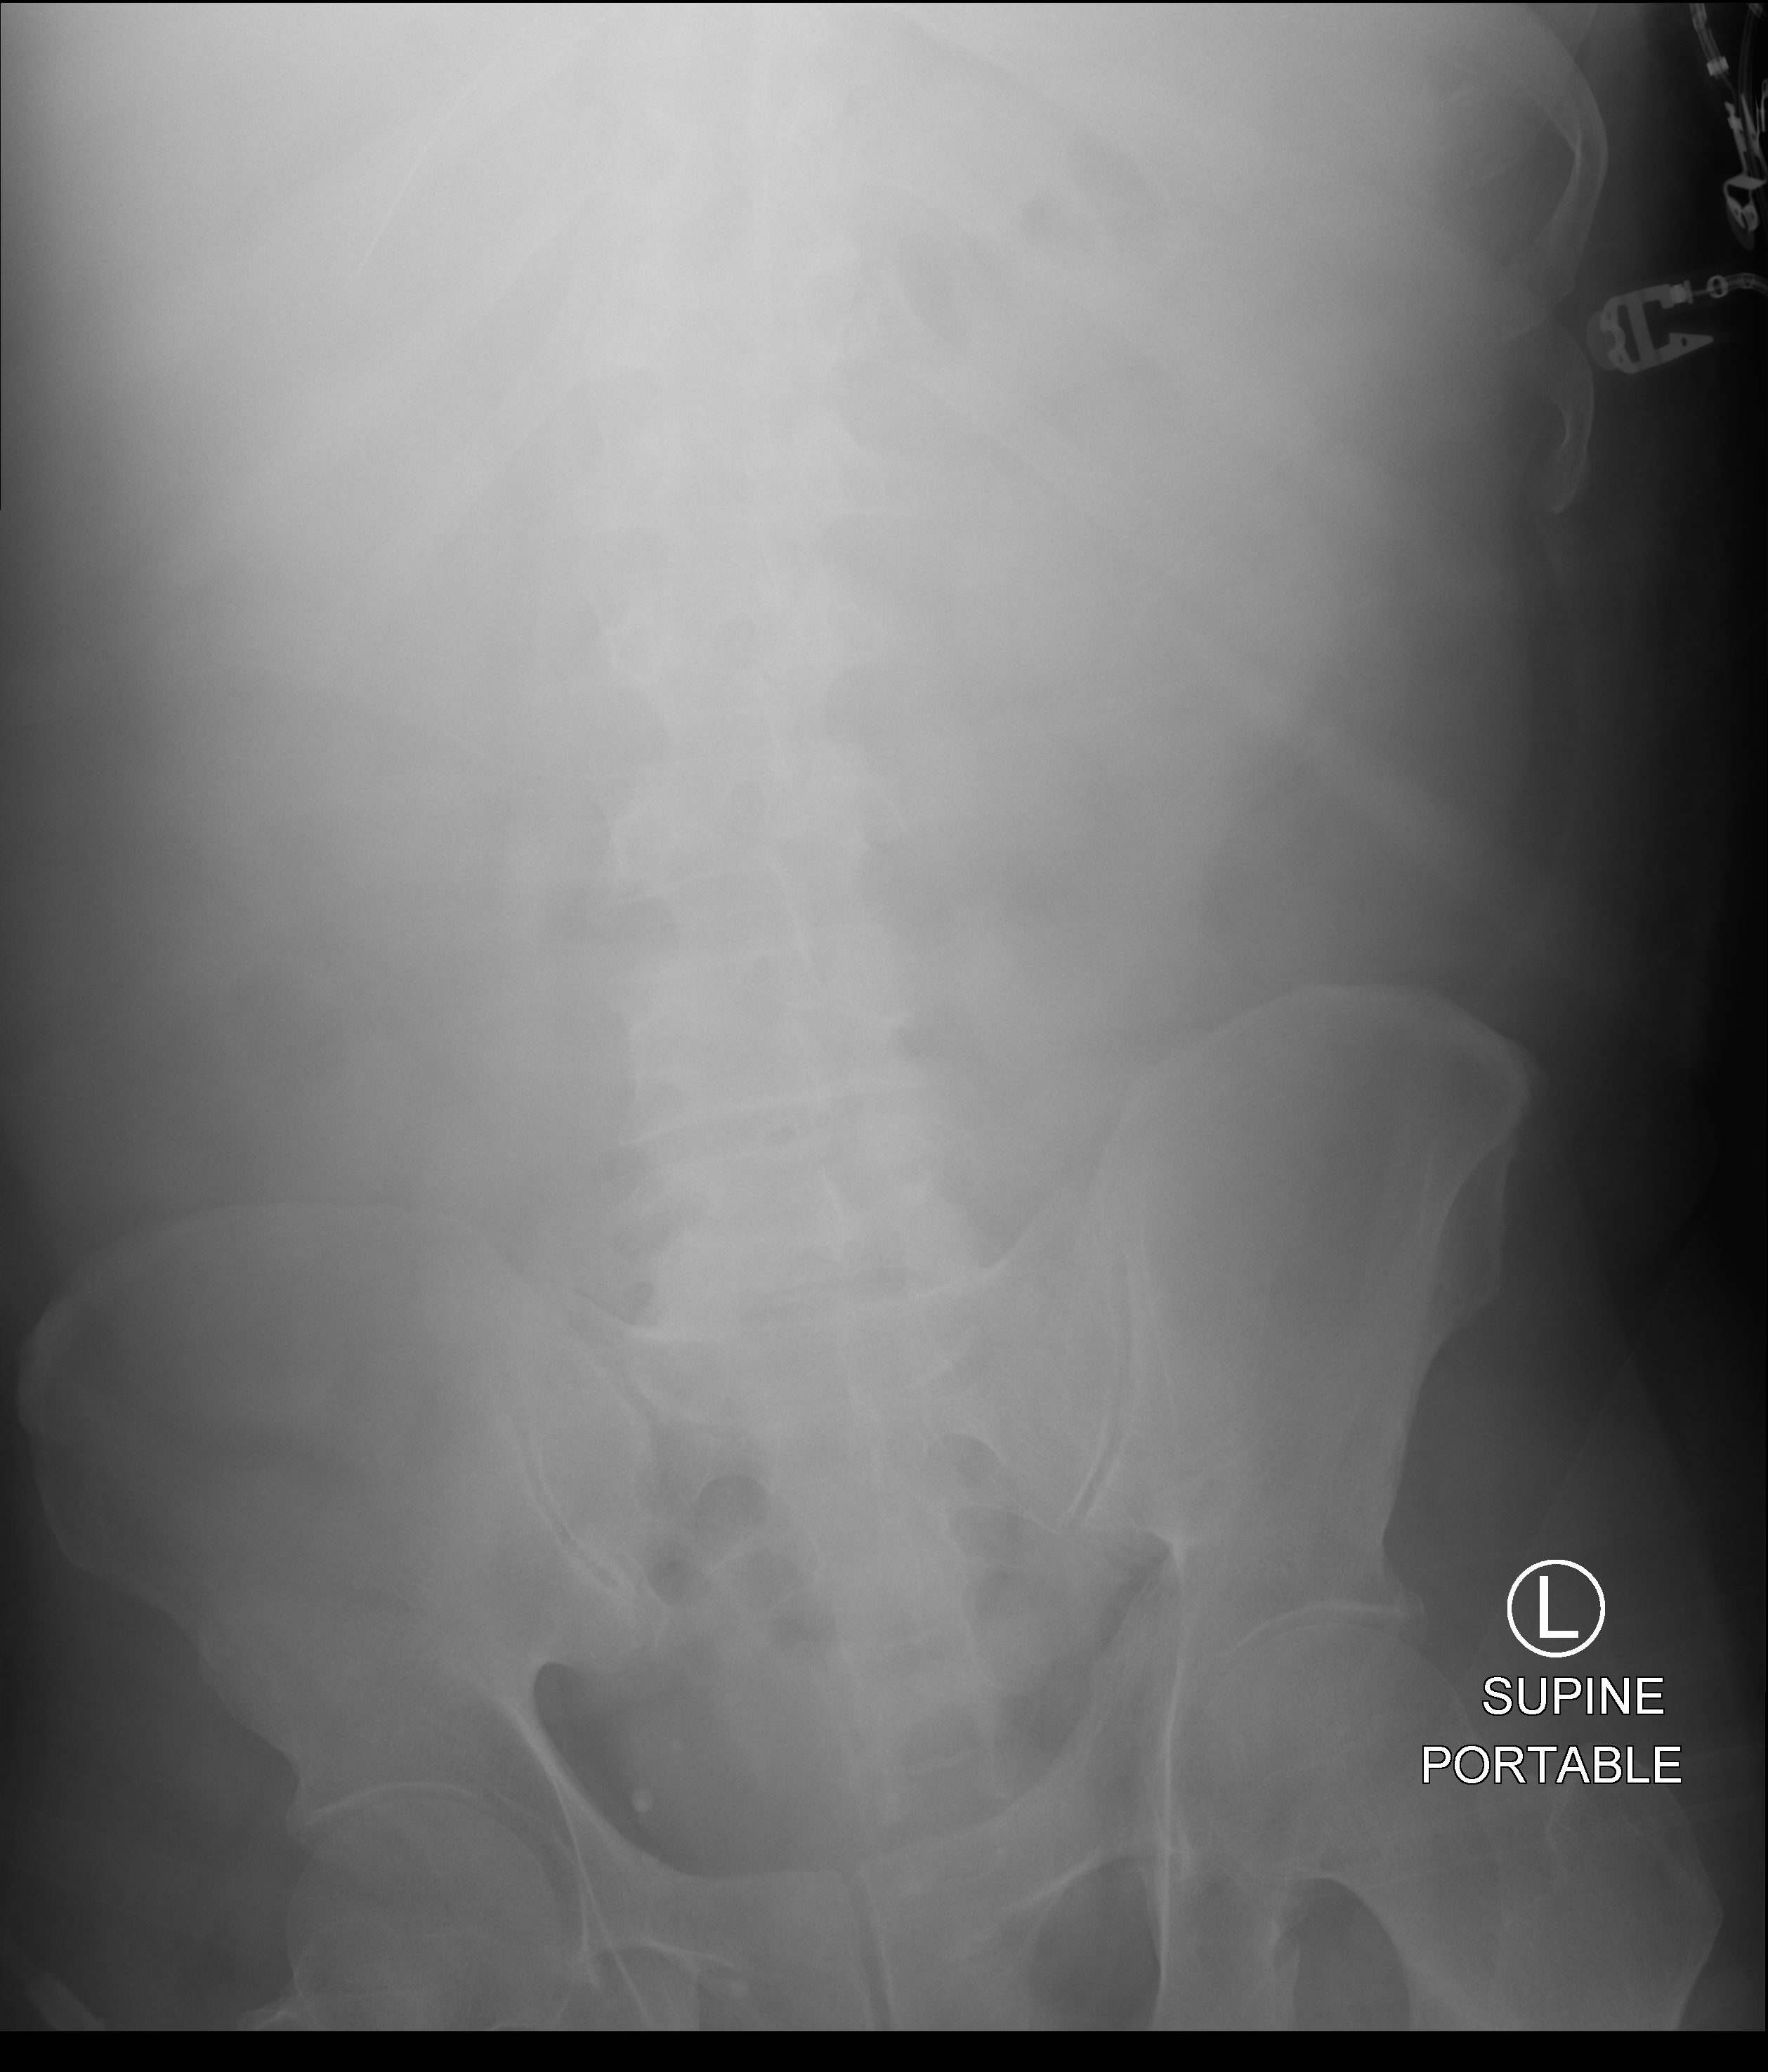
Bedside abdomen radiograph (computed radiography), anteroposterior (AP) projection. Patient hospitalised with COVID-19; male, aged 18–59 years.
Hospital-stay facts (about this admission, not read from this image; timing relative to this image not recorded):
- admitted to intensive care during this hospital stay: yes
- length of hospital stay: 48 days
- mechanically ventilated during this hospital stay: yes